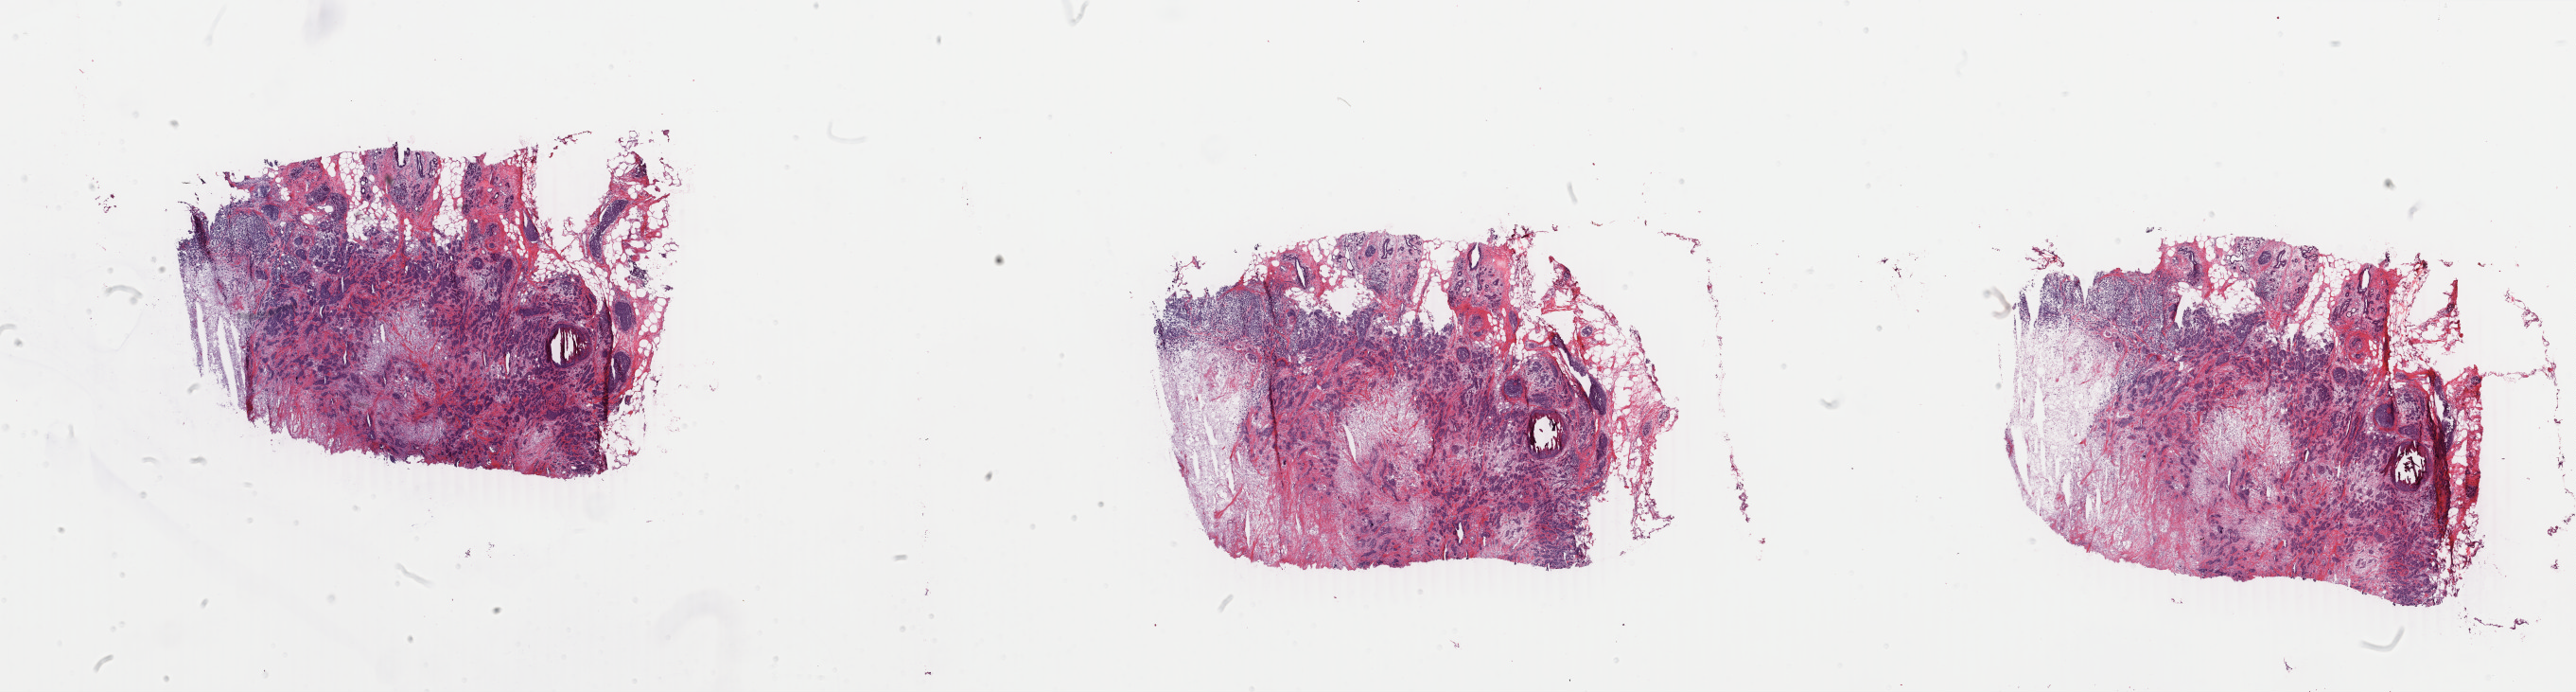
Digitized H&E tissue section (whole slide) — a low-resolution overview of the entire scanned area, about 43.3 x 11.6 mm; frozen section; primary tumour sample from the breast. Female, age 52 years at initial diagnosis. Pathologist review of this section (percent, as recorded): tumour cells 75%, tumour nuclei 70%, normal cells 15%, stromal cells 5%, necrosis 5%. Infiltration values recorded for this section: lymphocyte infiltration 0%, monocyte infiltration 0%, neutrophil infiltration 0%.
Pathologic diagnosis: Infiltrating duct carcinoma, NOS. AJCC pathologic stage: IIA. Laterality: left.